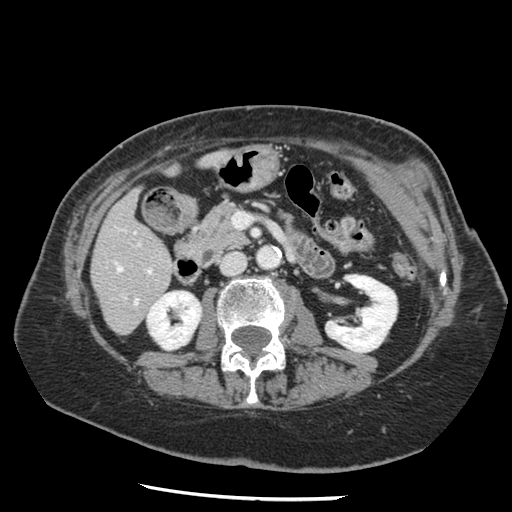
Contrast-enhanced abdominal CT, one axial slice. Slice 51 of 148 in the series (ordered by position). Soft-tissue window (W 400 / L 40 HU). 2.5 mm slice thickness. 512 × 512 image matrix, field of view 330 × 330 mm. Female patient, age 85 years. From the clinical record (not read from this slice): diagnosis: colorectal cancer liver metastases, imaged before liver resection; multiple liver metastases: no; largest metastasis: 0.9 cm; disease in both lobes: no.
Outlined on this slice (outlined manually by an expert reader):
- hepatic veins: box from (x=116, y=264) to (x=138, y=304) px
- liver: (x=92, y=154)–(x=222, y=334)
- planned liver remnant (the part of the liver to remain after resection): (x=94, y=154)–(x=222, y=334)